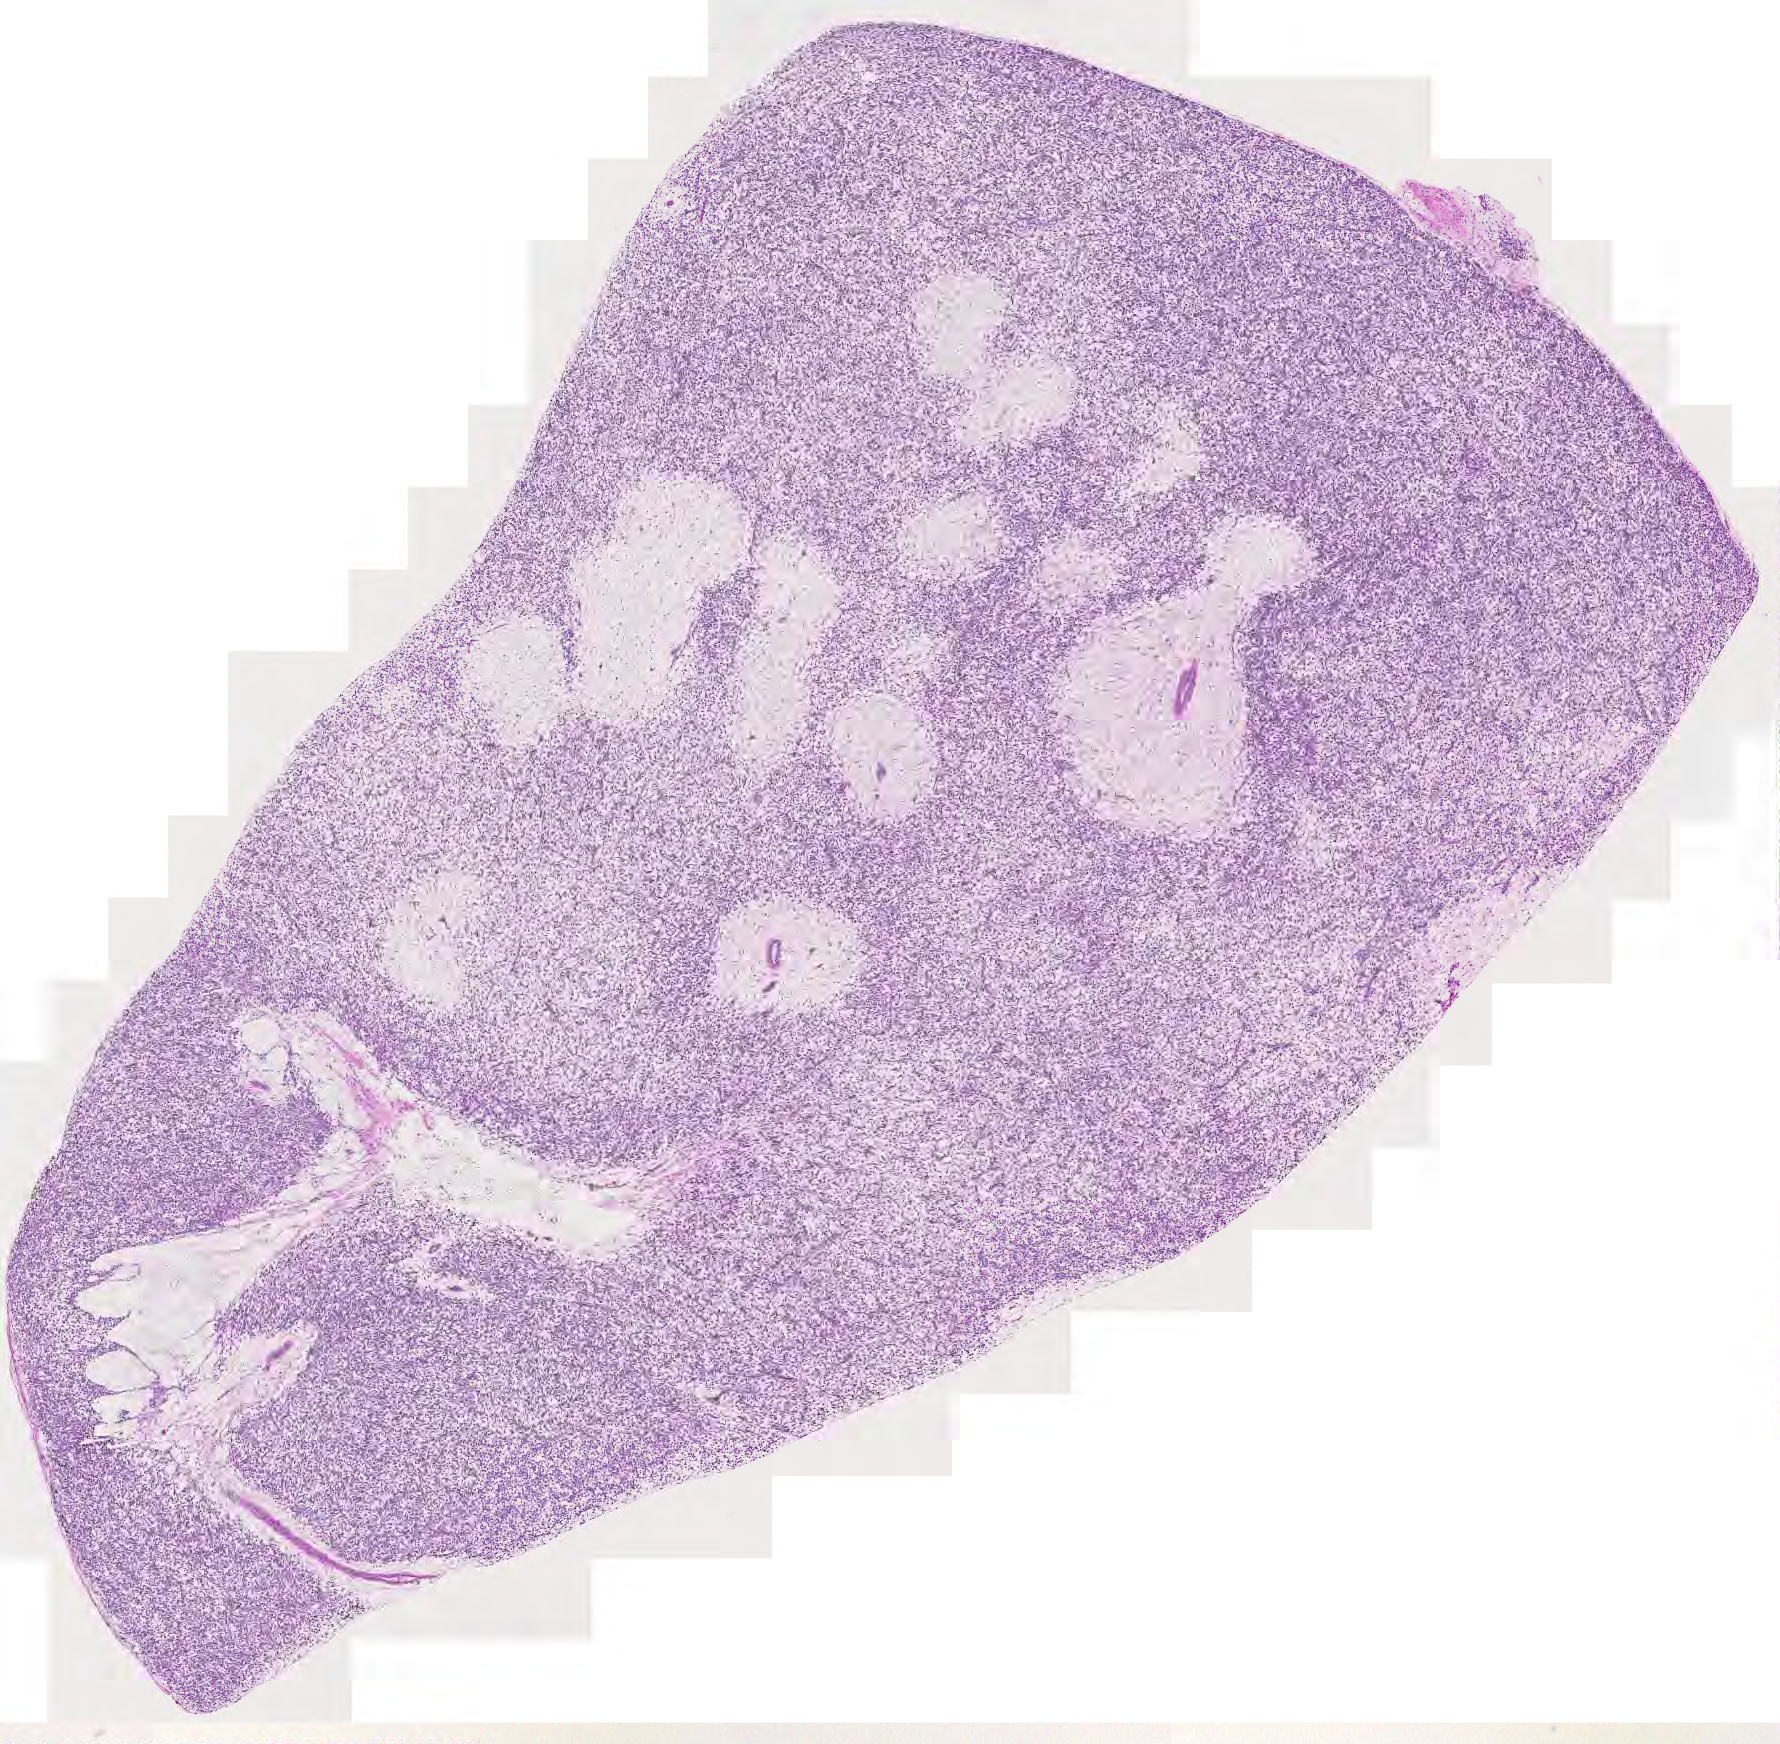
Whole-slide histology image, H&E, shown as a low-resolution overview of the whole scanned area (about 9.2 x 9.0 mm, acquisition: 20x scan), tumour tissue sample. Patient: female, age 41 years.
• patient diagnosis (cohort enrolment): sarcoma (site not recorded at cohort level)
• primary tumour site (as recorded): lower extremity